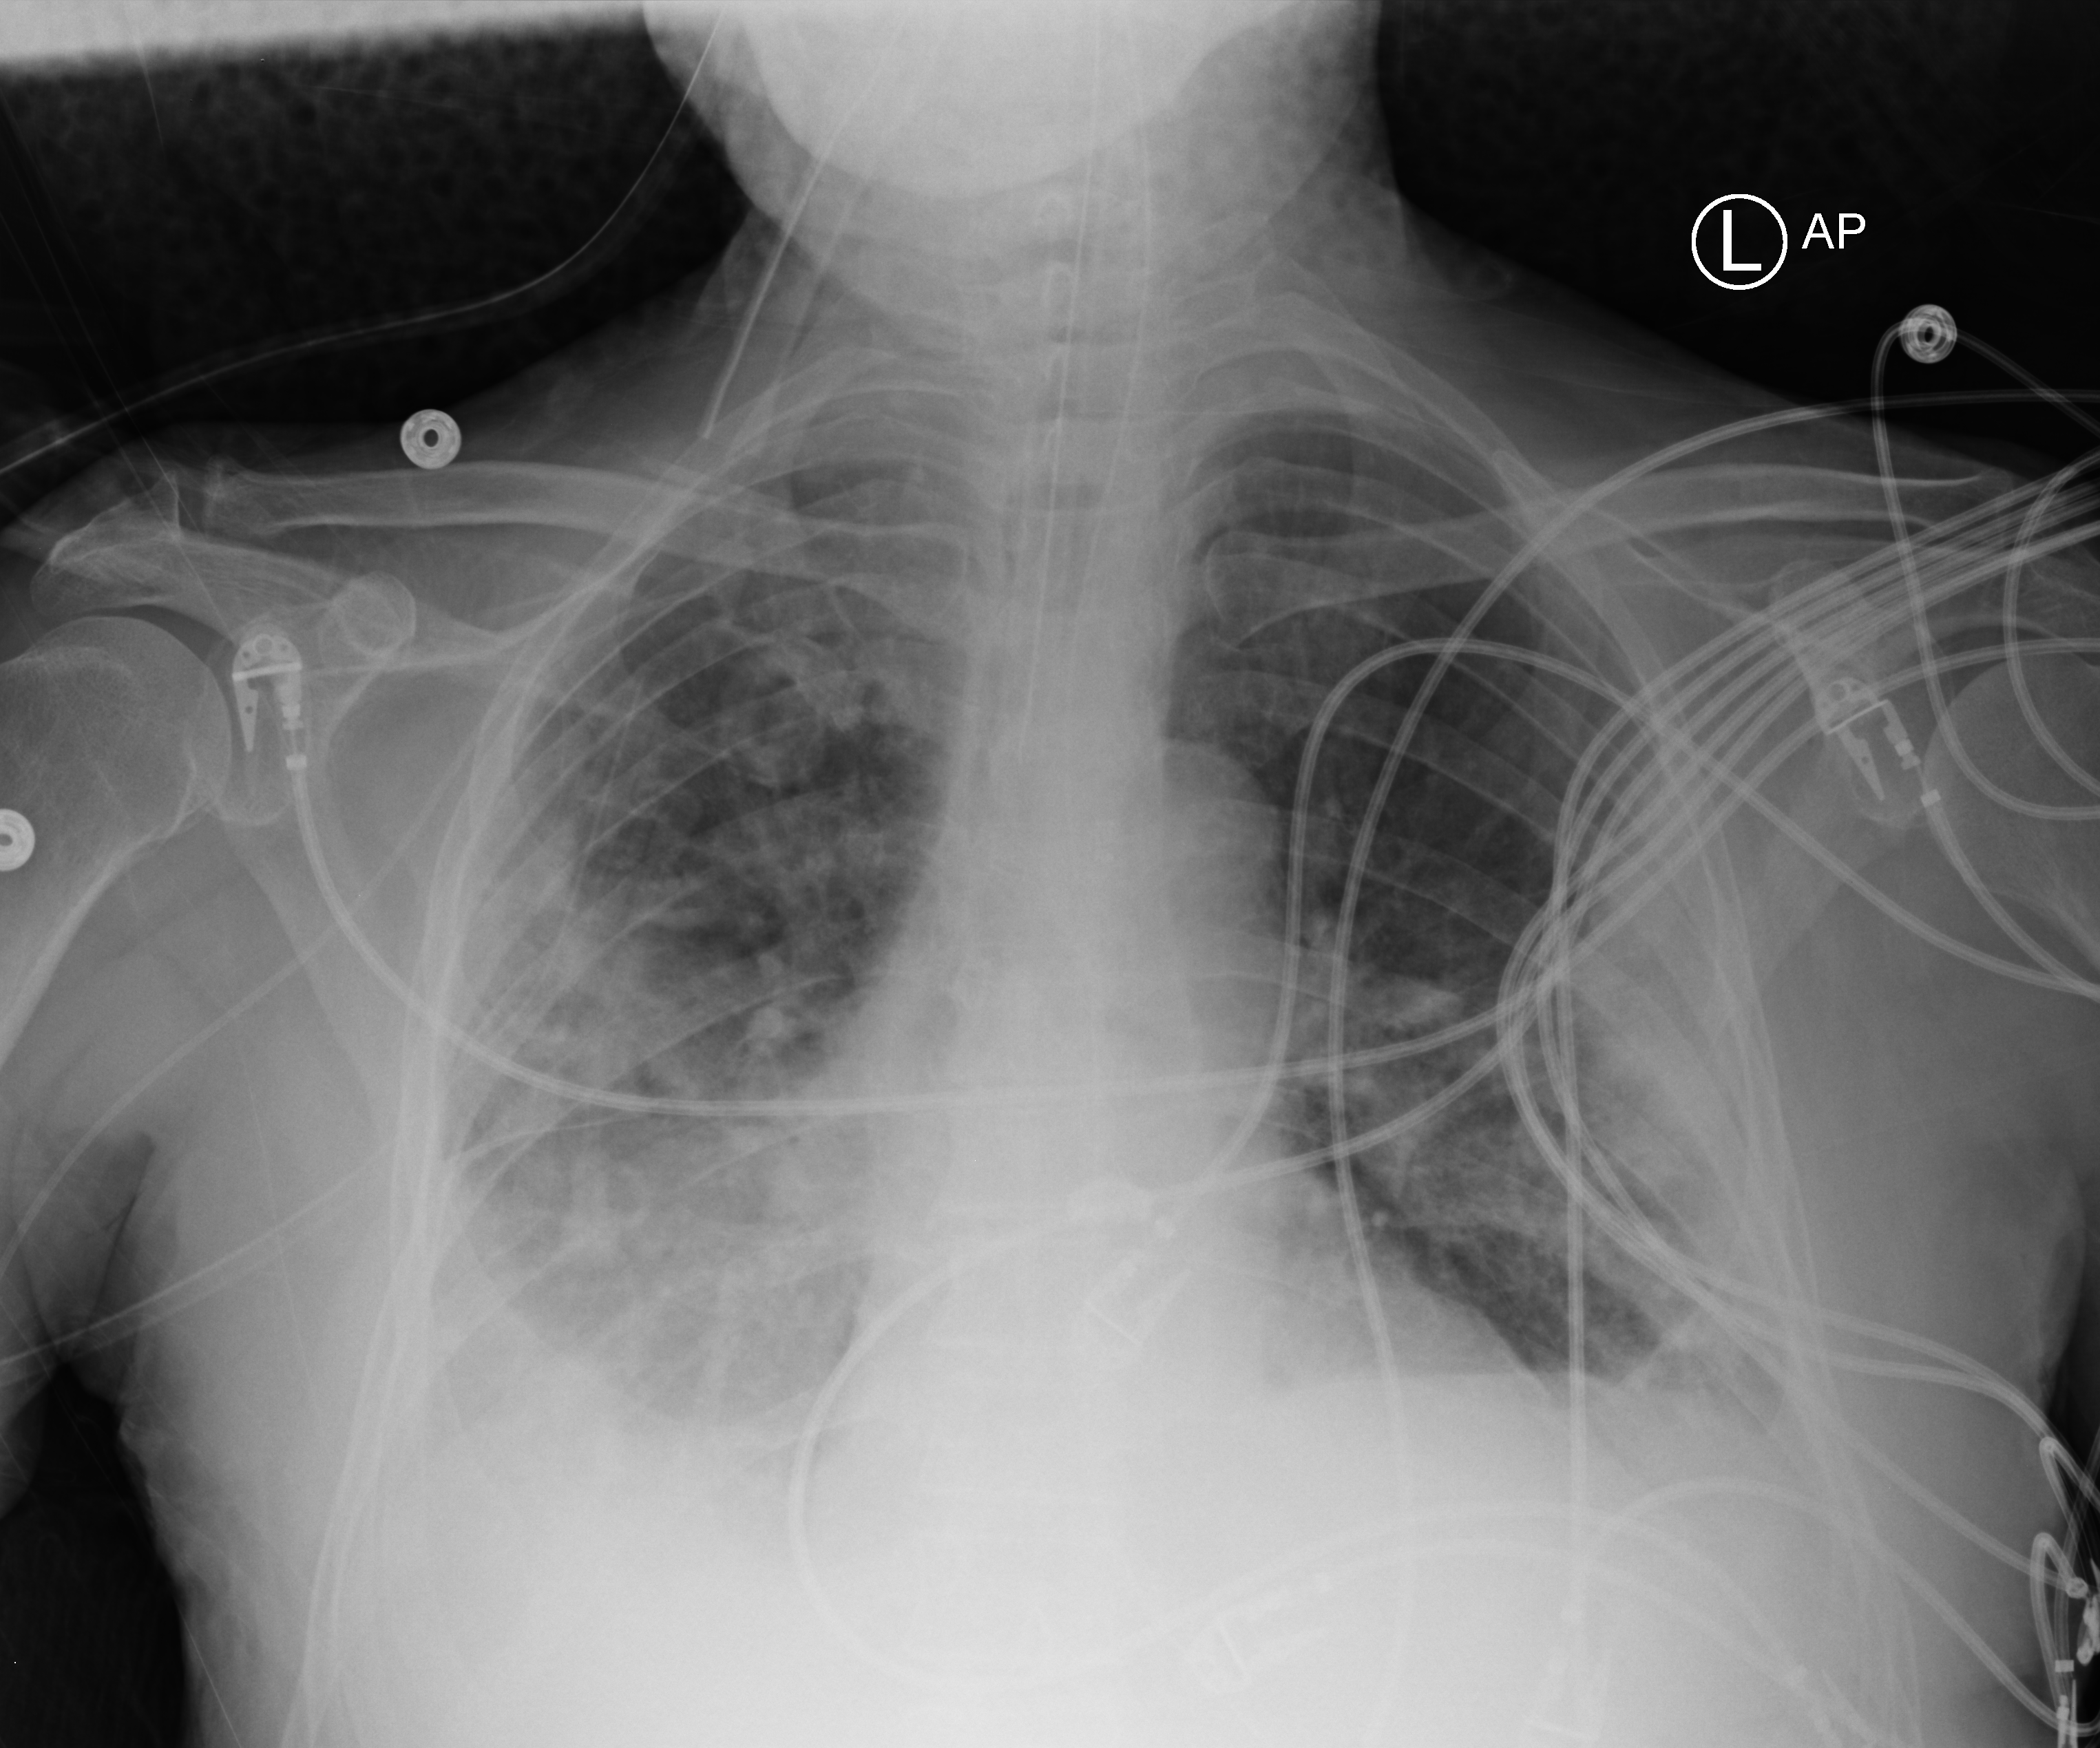
Portable chest radiograph. Male patient hospitalised with COVID-19, age 75–90 years.
Hospital-stay facts (about this admission, not read from this image; timing relative to this image not recorded):
- length of hospital stay: 70 days
- mechanically ventilated during this hospital stay: yes